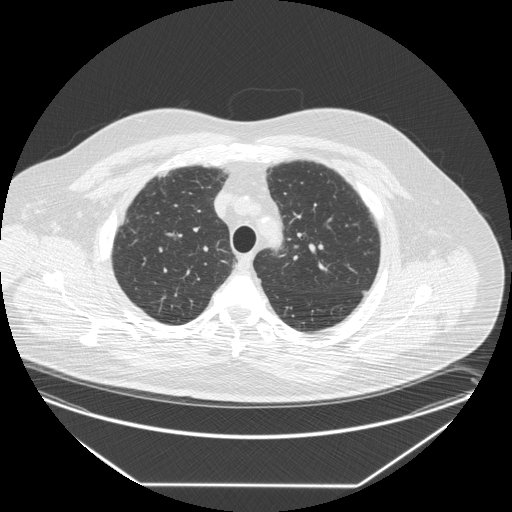
Low-dose screening chest CT, one axial slice; position 210 of 258 along the scan axis; reconstruction kernel STANDARD; lung window (W 1500 / L -600 HU); 2.5 mm slice thickness; 512 × 512 image matrix.
Annotated regions visible in this slice (outlined manually by an expert reader):
- lesion 1 (tumor, upper lobe of right lung): bounding box [x1, y1, x2, y2] px = [233, 263, 237, 268]